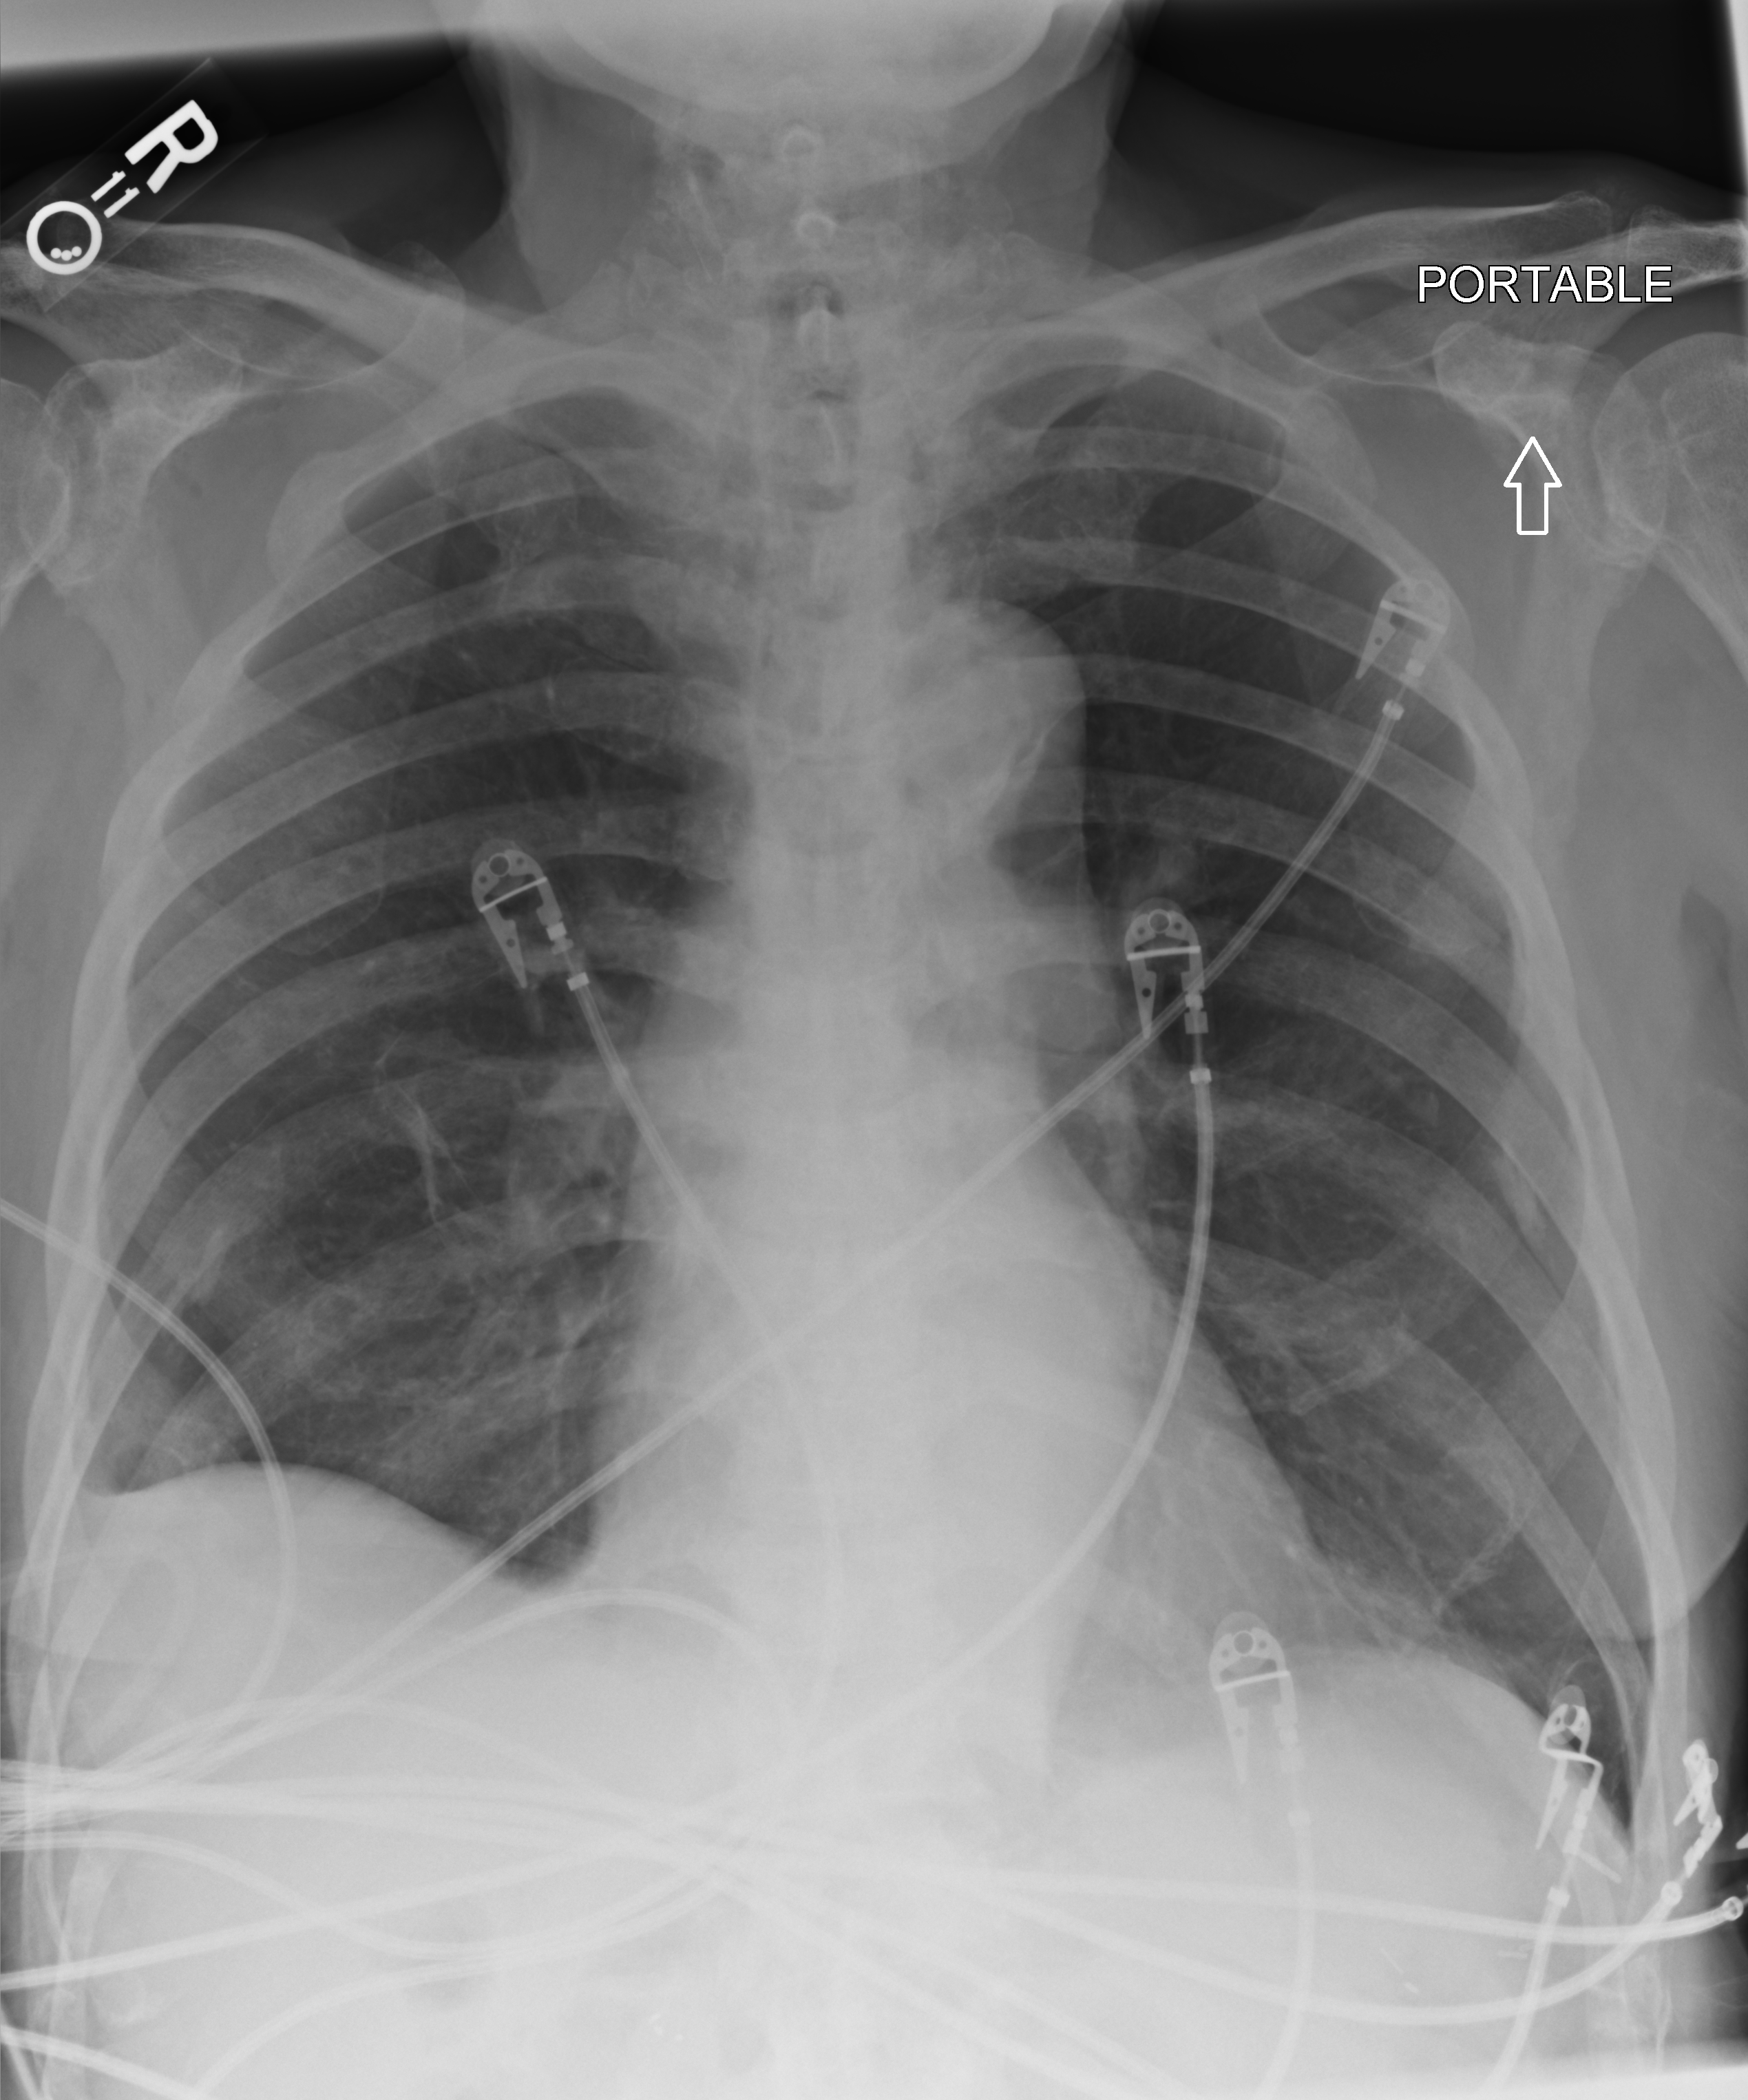
Portable chest radiograph; anteroposterior (AP) projection. Patient hospitalised with COVID-19; male, aged 75–90 years.
Admission-level facts for this patient (not findings on this image; timing relative to this image not recorded): length of hospital stay: 12 days; mechanically ventilated during this hospital stay: no; admitted to intensive care during this hospital stay: no.